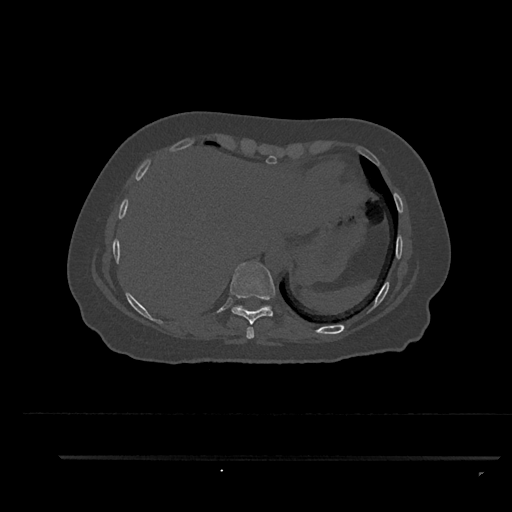
CT including the spine, one axial slice; slice 407 of 797 in the series (ordered by position); bone window (W 1800 / L 400 HU); 512 × 512 image matrix, field of view 408 × 408 mm. Female patient, age 44 years. From the clinical record (not read from this slice): primary cancer: renal; vertebrae with lytic lesions (as recorded): L1.
Outlined on this slice (semi-automatically segmented with operator editing):
- T10 vertebra: box from (x=236, y=306) to (x=272, y=308) px
- T8 vertebra: (x=246, y=326)–(x=255, y=339)
- T9 vertebra: (x=230, y=262)–(x=275, y=325)